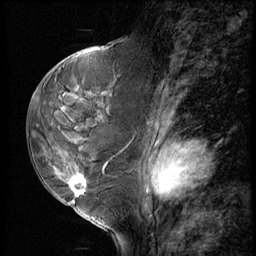
Breast MRI (dynamic contrast-enhanced), one sagittal slice. Slice 31 of 60 in the series (ordered by position). 3 images stored at this slice position (order not interpretable as contrast timing). 1.5 T. TE 4.2 ms, TR 8.9 ms. 2.5 mm slice thickness. 256 × 256 image matrix. Female patient, age 50 years. From the clinical record (not read from this slice): setting: breast cancer imaged before/during neoadjuvant chemotherapy; receptor status: HR-positive, HER2-negative.
Annotated regions visible in this slice (semi-automatically segmented with operator editing):
- analysis volume of interest (the breast-tissue region the enhancement analysis was run in; not a lesion): bounding box <38,102,118,213> (left, top, right, bottom; pixels)
- tumour enhancement mask (voxels above the 140 % enhancement threshold inside the analysis volume of interest): <70,176,88,195>